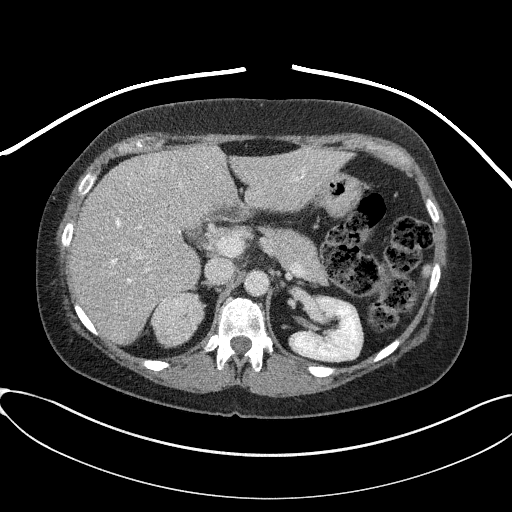
Contrast-enhanced abdominal CT, one axial slice; slice 52 of 95 in the series (ordered by position); reconstruction kernel I41f/2; 100 kVp; intravenous contrast given; soft-tissue window (W 400 / L 40 HU); 3 mm slice thickness; 512 × 512 image matrix, field of view 410 × 410 mm. Female patient, age 46 years. From the clinical record (not read from this slice): diagnosis: adrenocortical carcinoma; tumour side: right adrenal; tumour size at pathology: 7.2 cm; Ki-67 index: 50 %; stage (as recorded): 4.
Annotated regions visible in this slice (semi-automatic segmentation, software-assisted and operator-edited):
- mass: bounding box (x1, y1, x2, y2) in pixels: (152, 293, 203, 345)